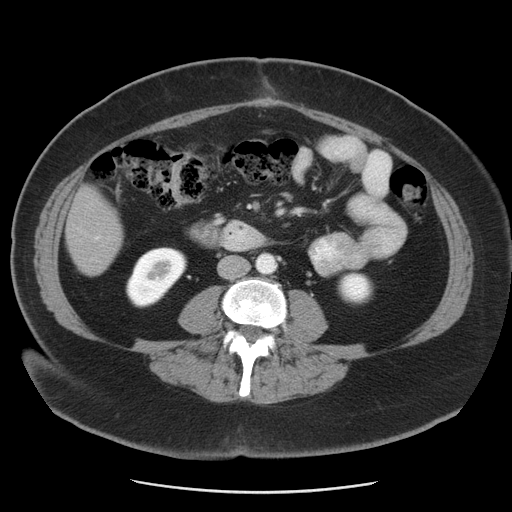
Contrast-enhanced abdominal CT, one axial slice; slice 7 of 55 in the series (ordered by position); reconstruction kernel STANDARD; 120 kVp; soft-tissue window (W 400 / L 40 HU); 5 mm slice thickness; 512 × 512 image matrix, field of view 380 × 380 mm. Female patient, age 52 years. From the clinical record (not read from this slice): diagnosis: colorectal cancer liver metastases, imaged before liver resection; multiple liver metastases: yes; largest metastasis: 2.5 cm; disease in both lobes: yes.
Structures marked on this image (outlined manually by an expert reader):
- liver: bounding box [x1, y1, x2, y2] px = [66, 185, 123, 276]
- planned liver remnant (the part of the liver to remain after resection): [65, 198, 122, 275]
- portal vein (with intrahepatic branches): [91, 203, 110, 241]